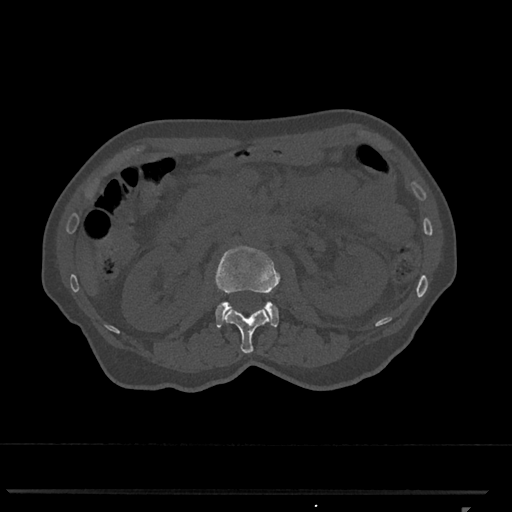
CT including the spine, one axial slice. Position 371 of 793 along the scan axis. Reconstruction kernel Br40s/3. Bone window (W 1800 / L 400 HU). 0.5 mm slice thickness. 512 × 512 image matrix, field of view 380 × 380 mm. Female patient, age 62 years. From the clinical record (not read from this slice): primary cancer: renal.
Annotated regions visible in this slice (semi-automatically segmented with operator editing):
- L1 vertebra: box from (x=223, y=306) to (x=271, y=354) px
- L2 vertebra: (x=215, y=246)–(x=280, y=328)